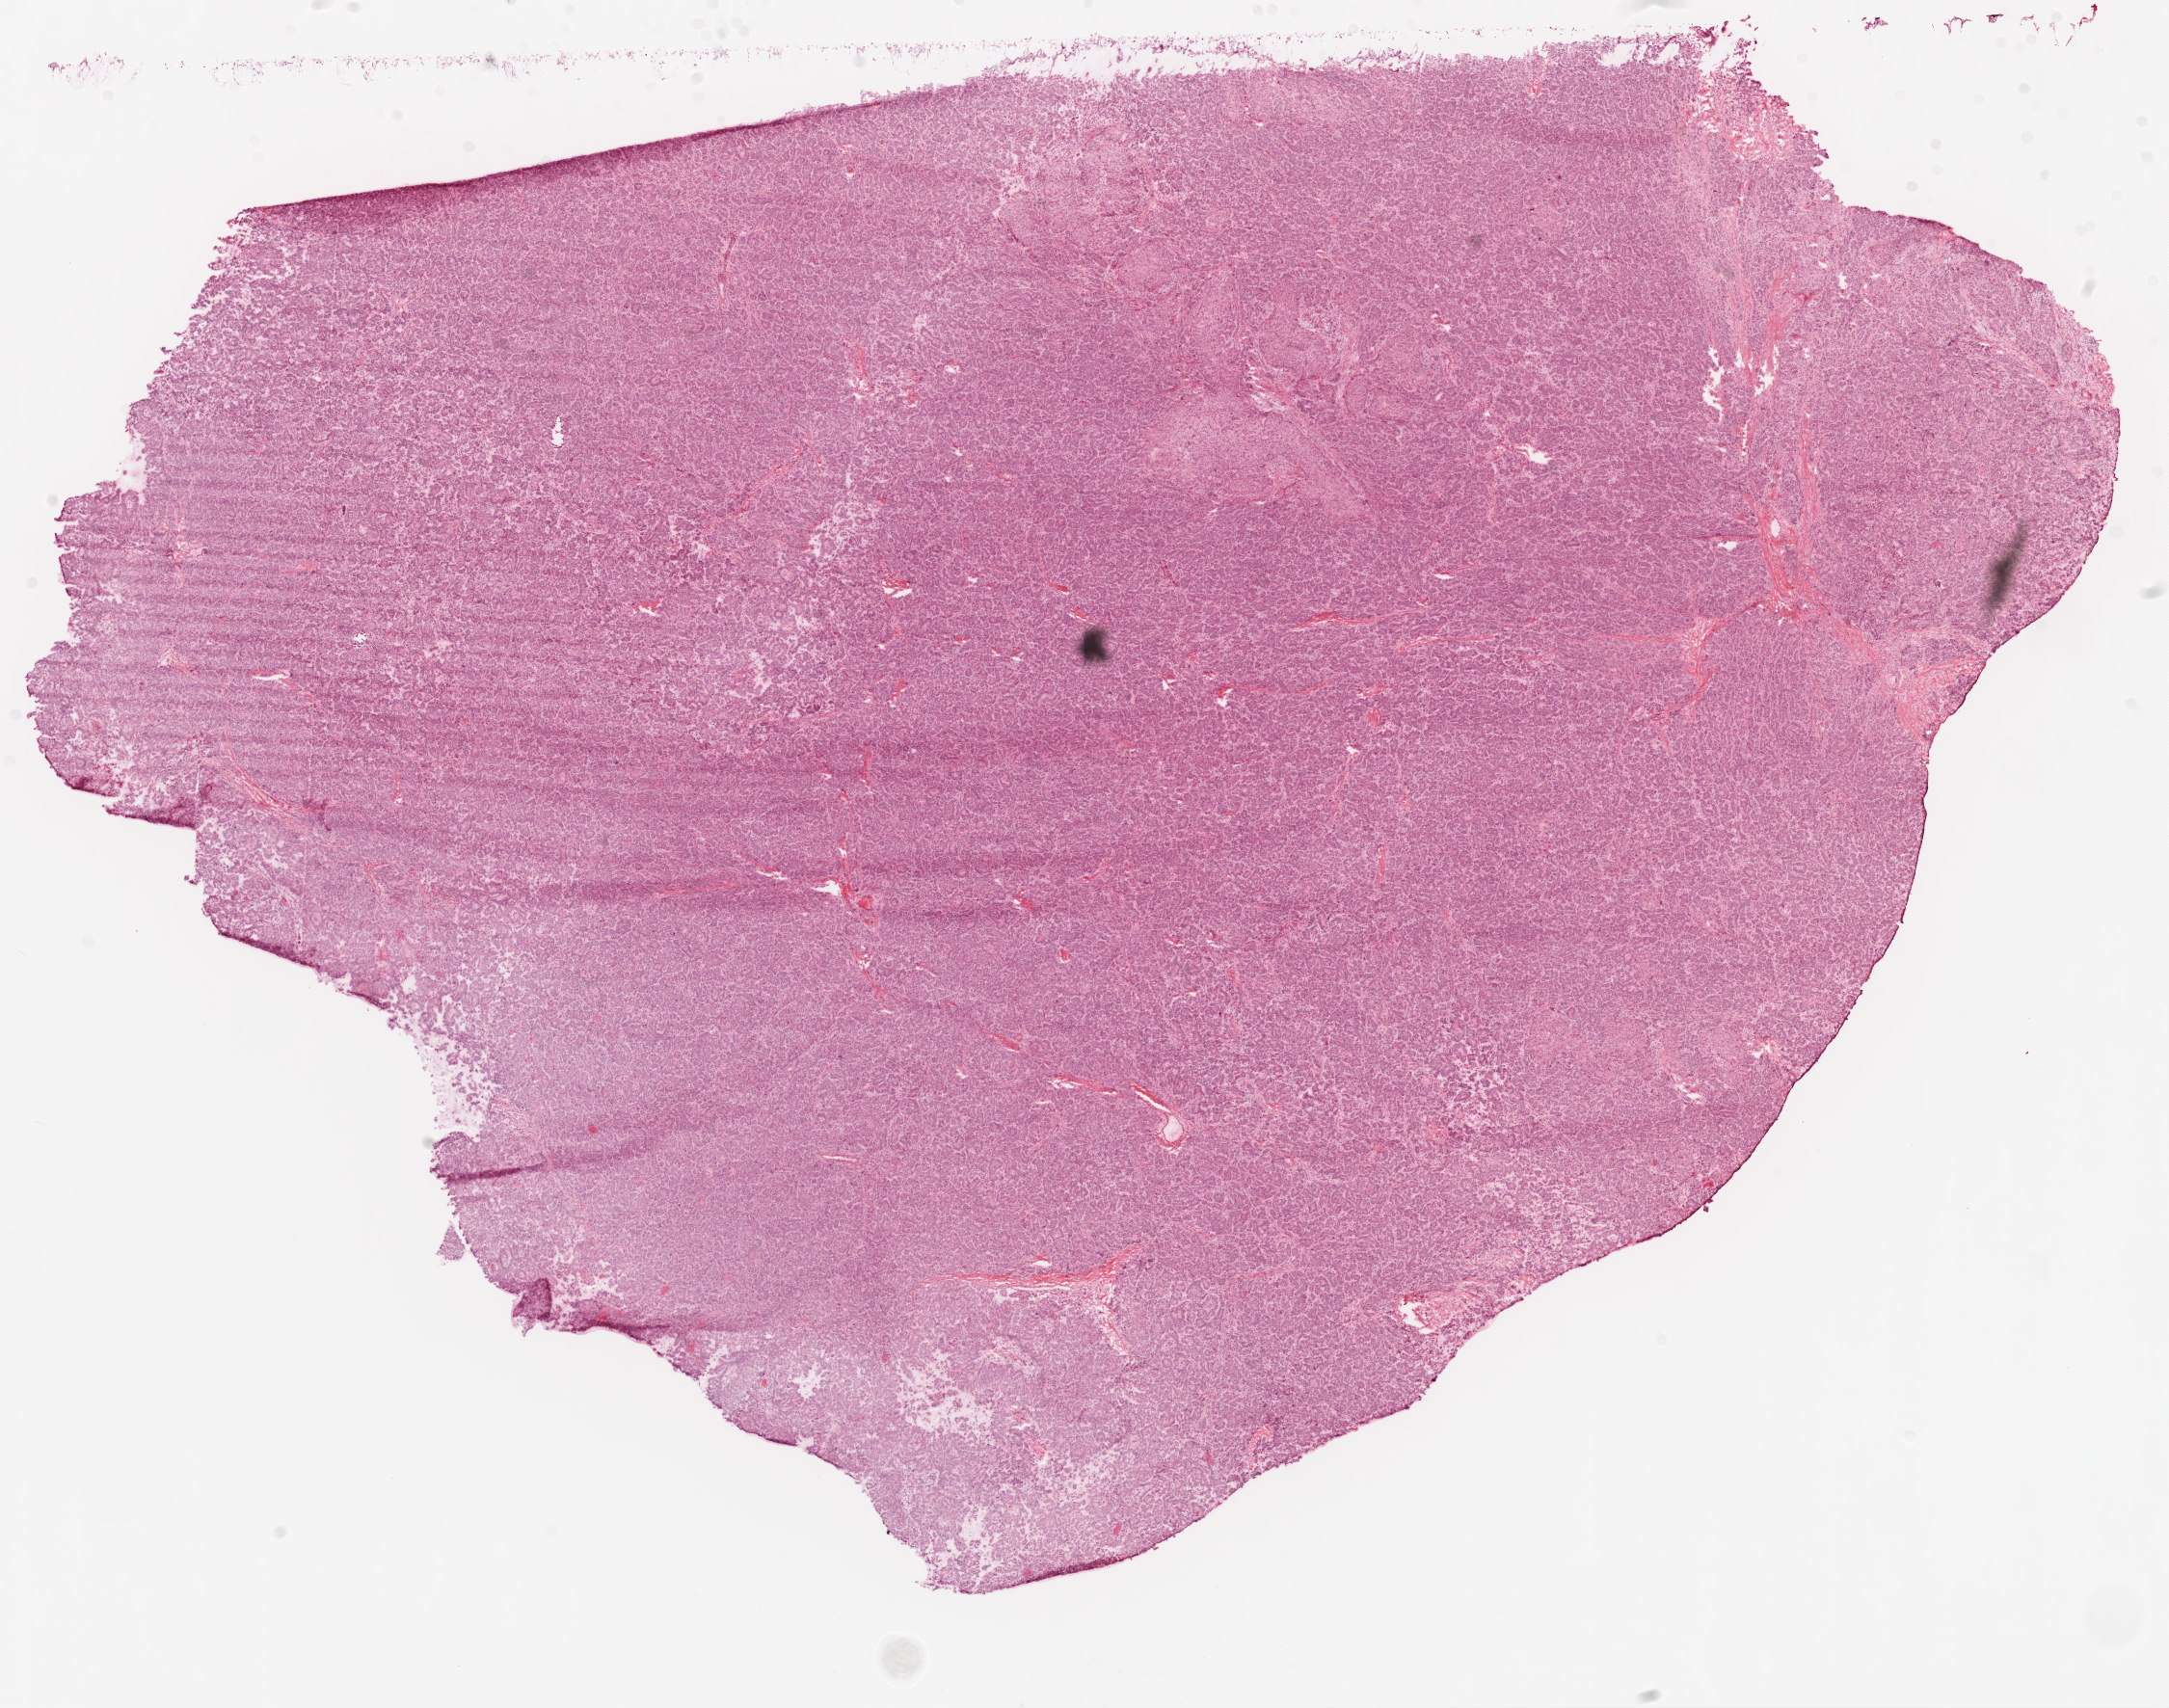
Digitized H&E tissue section (whole slide), shown as a low-resolution overview of the whole scanned area (about 18.1 x 14.2 mm, slide scanned at 20x); frozen section from the top of the tissue portion; primary tumour sample from the ovary. Patient: female, age at initial diagnosis 71 years. Histologic grade: G3 (poorly differentiated). Composition of this section per pathologist review: tumour cells 94%, tumour nuclei 95%, normal cells 1%, stromal cells 4%, necrosis 1%.
• diagnosis: Serous cystadenocarcinoma, NOS
• FIGO stage: IV